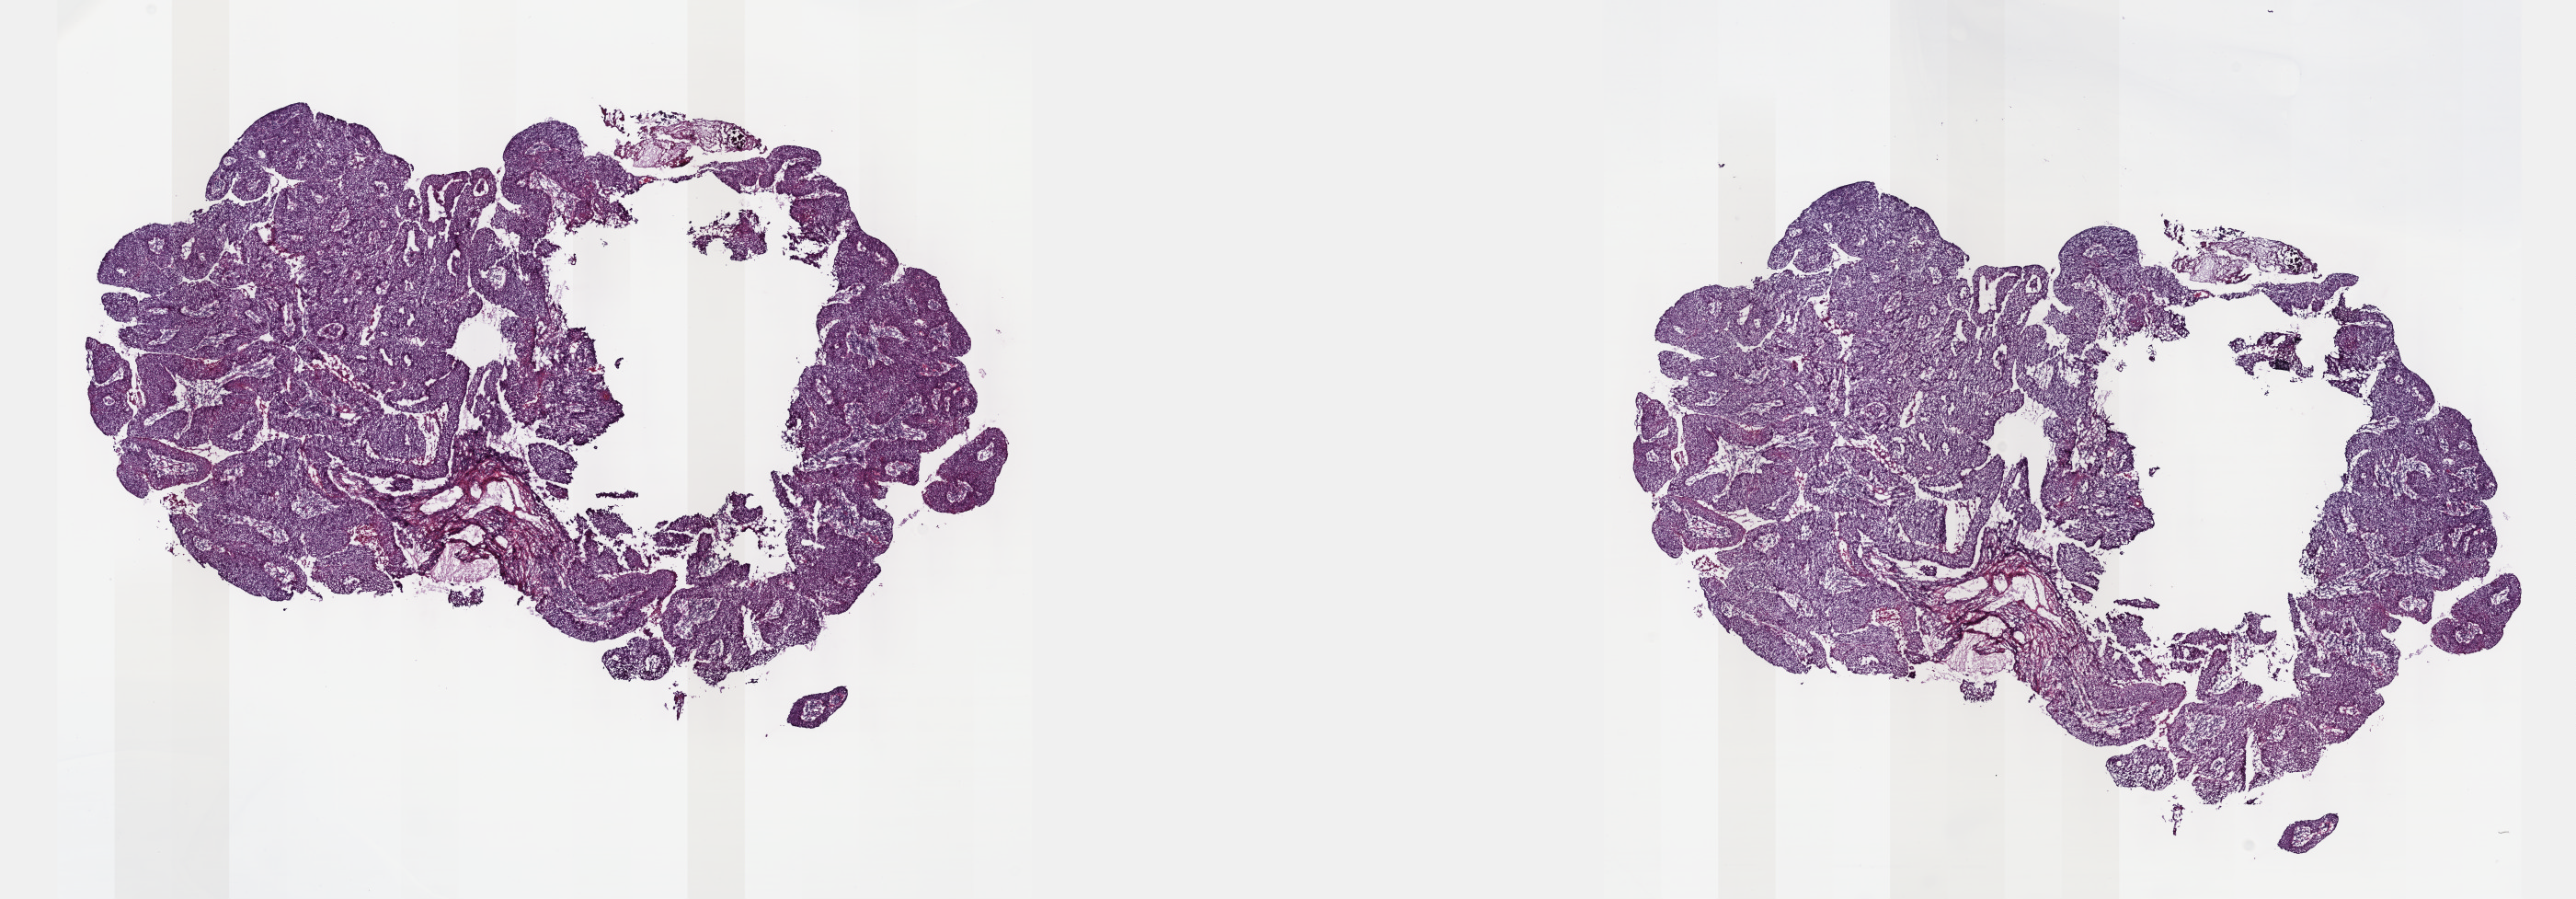
H&E-stained whole-slide image, shown as a low-resolution overview of the whole scanned area (about 22.6 x 7.9 mm), frozen section, sample: primary tumour, cervix. Female, age 43 years at initial diagnosis. Histologic grade: GX (grade cannot be assessed). Pathologist review of this section (percent, as recorded): tumour cells 80%, tumour nuclei 80%, normal cells 0%, stromal cells 20%, necrosis 0%. Inflammatory infiltration, as recorded: lymphocyte infiltration 10%, monocyte infiltration 0%, neutrophil infiltration 0%.
FIGO stage: IB2. Diagnosis: Squamous cell carcinoma, NOS (cervix uteri).